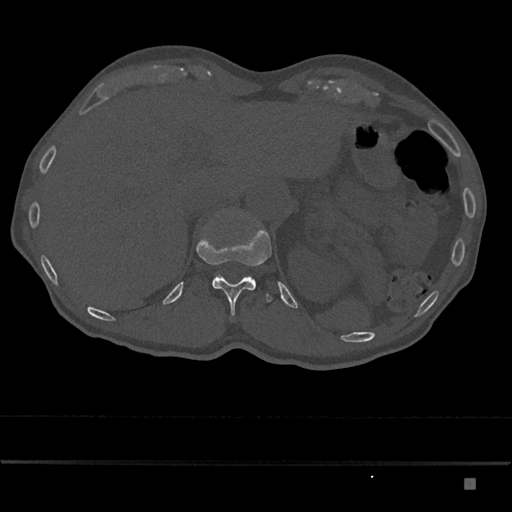
CT including the spine, one axial slice. Slice 604 of 797 in the series (ordered by position). Reconstruction kernel Br40s/3. Bone window (W 1800 / L 400 HU). 0.5 mm slice thickness. 512 × 512 image matrix, field of view 390 × 390 mm. Patient: male, 72 years. From the clinical record (not read from this slice): primary cancer: prostate.
Annotated regions visible in this slice (semi-automatic segmentation, software-assisted and operator-edited):
- T12 vertebra: box from (x=196, y=229) to (x=272, y=316) px